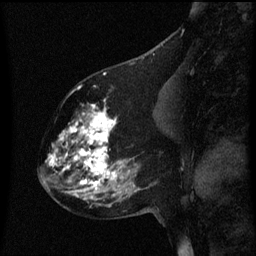
Breast MRI (dynamic contrast-enhanced), one sagittal slice; slice 28 of 60 in the series (ordered by position); dynamic contrast-enhanced series, image 2 of 3 at this slice position (ordered by acquisition); 1.5 T; TE 4.2 ms, TR 8 ms; 256 × 256 image matrix, field of view 200 × 200 mm. Female patient, age 60 years.
Structures marked on this image (semi-automatically segmented with operator editing):
- analysis volume of interest (the breast-tissue region the enhancement analysis was run in; not a lesion): bounding box [x1, y1, x2, y2] px = [49, 102, 158, 197]
- tumour enhancement mask (voxels above the 70 % enhancement threshold inside the analysis volume of interest): [49, 104, 123, 197]